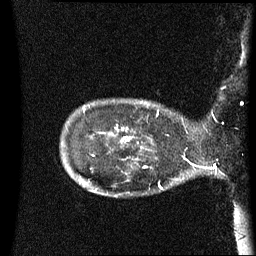
Breast MRI (dynamic contrast-enhanced), one sagittal slice; position 11 of 60 along the scan axis; dynamic contrast-enhanced series, image 2 of 3 at this slice position (ordered by acquisition); 1.5 T; TE 4.2 ms, TR 8.4 ms; 2.5 mm slice thickness; 256 × 256 image matrix. Patient: female, 41 years. From the clinical record (not read from this slice): setting: breast cancer imaged before/during neoadjuvant chemotherapy; receptor status: HER2-positive.
Outlined on this slice (semi-automatically segmented with operator editing):
- analysis volume of interest (the breast-tissue region the enhancement analysis was run in; not a lesion): bounding box [x1, y1, x2, y2] px = [122, 100, 195, 137]
- tumour enhancement mask (voxels above the 70 % enhancement threshold inside the analysis volume of interest): [125, 110, 159, 131]